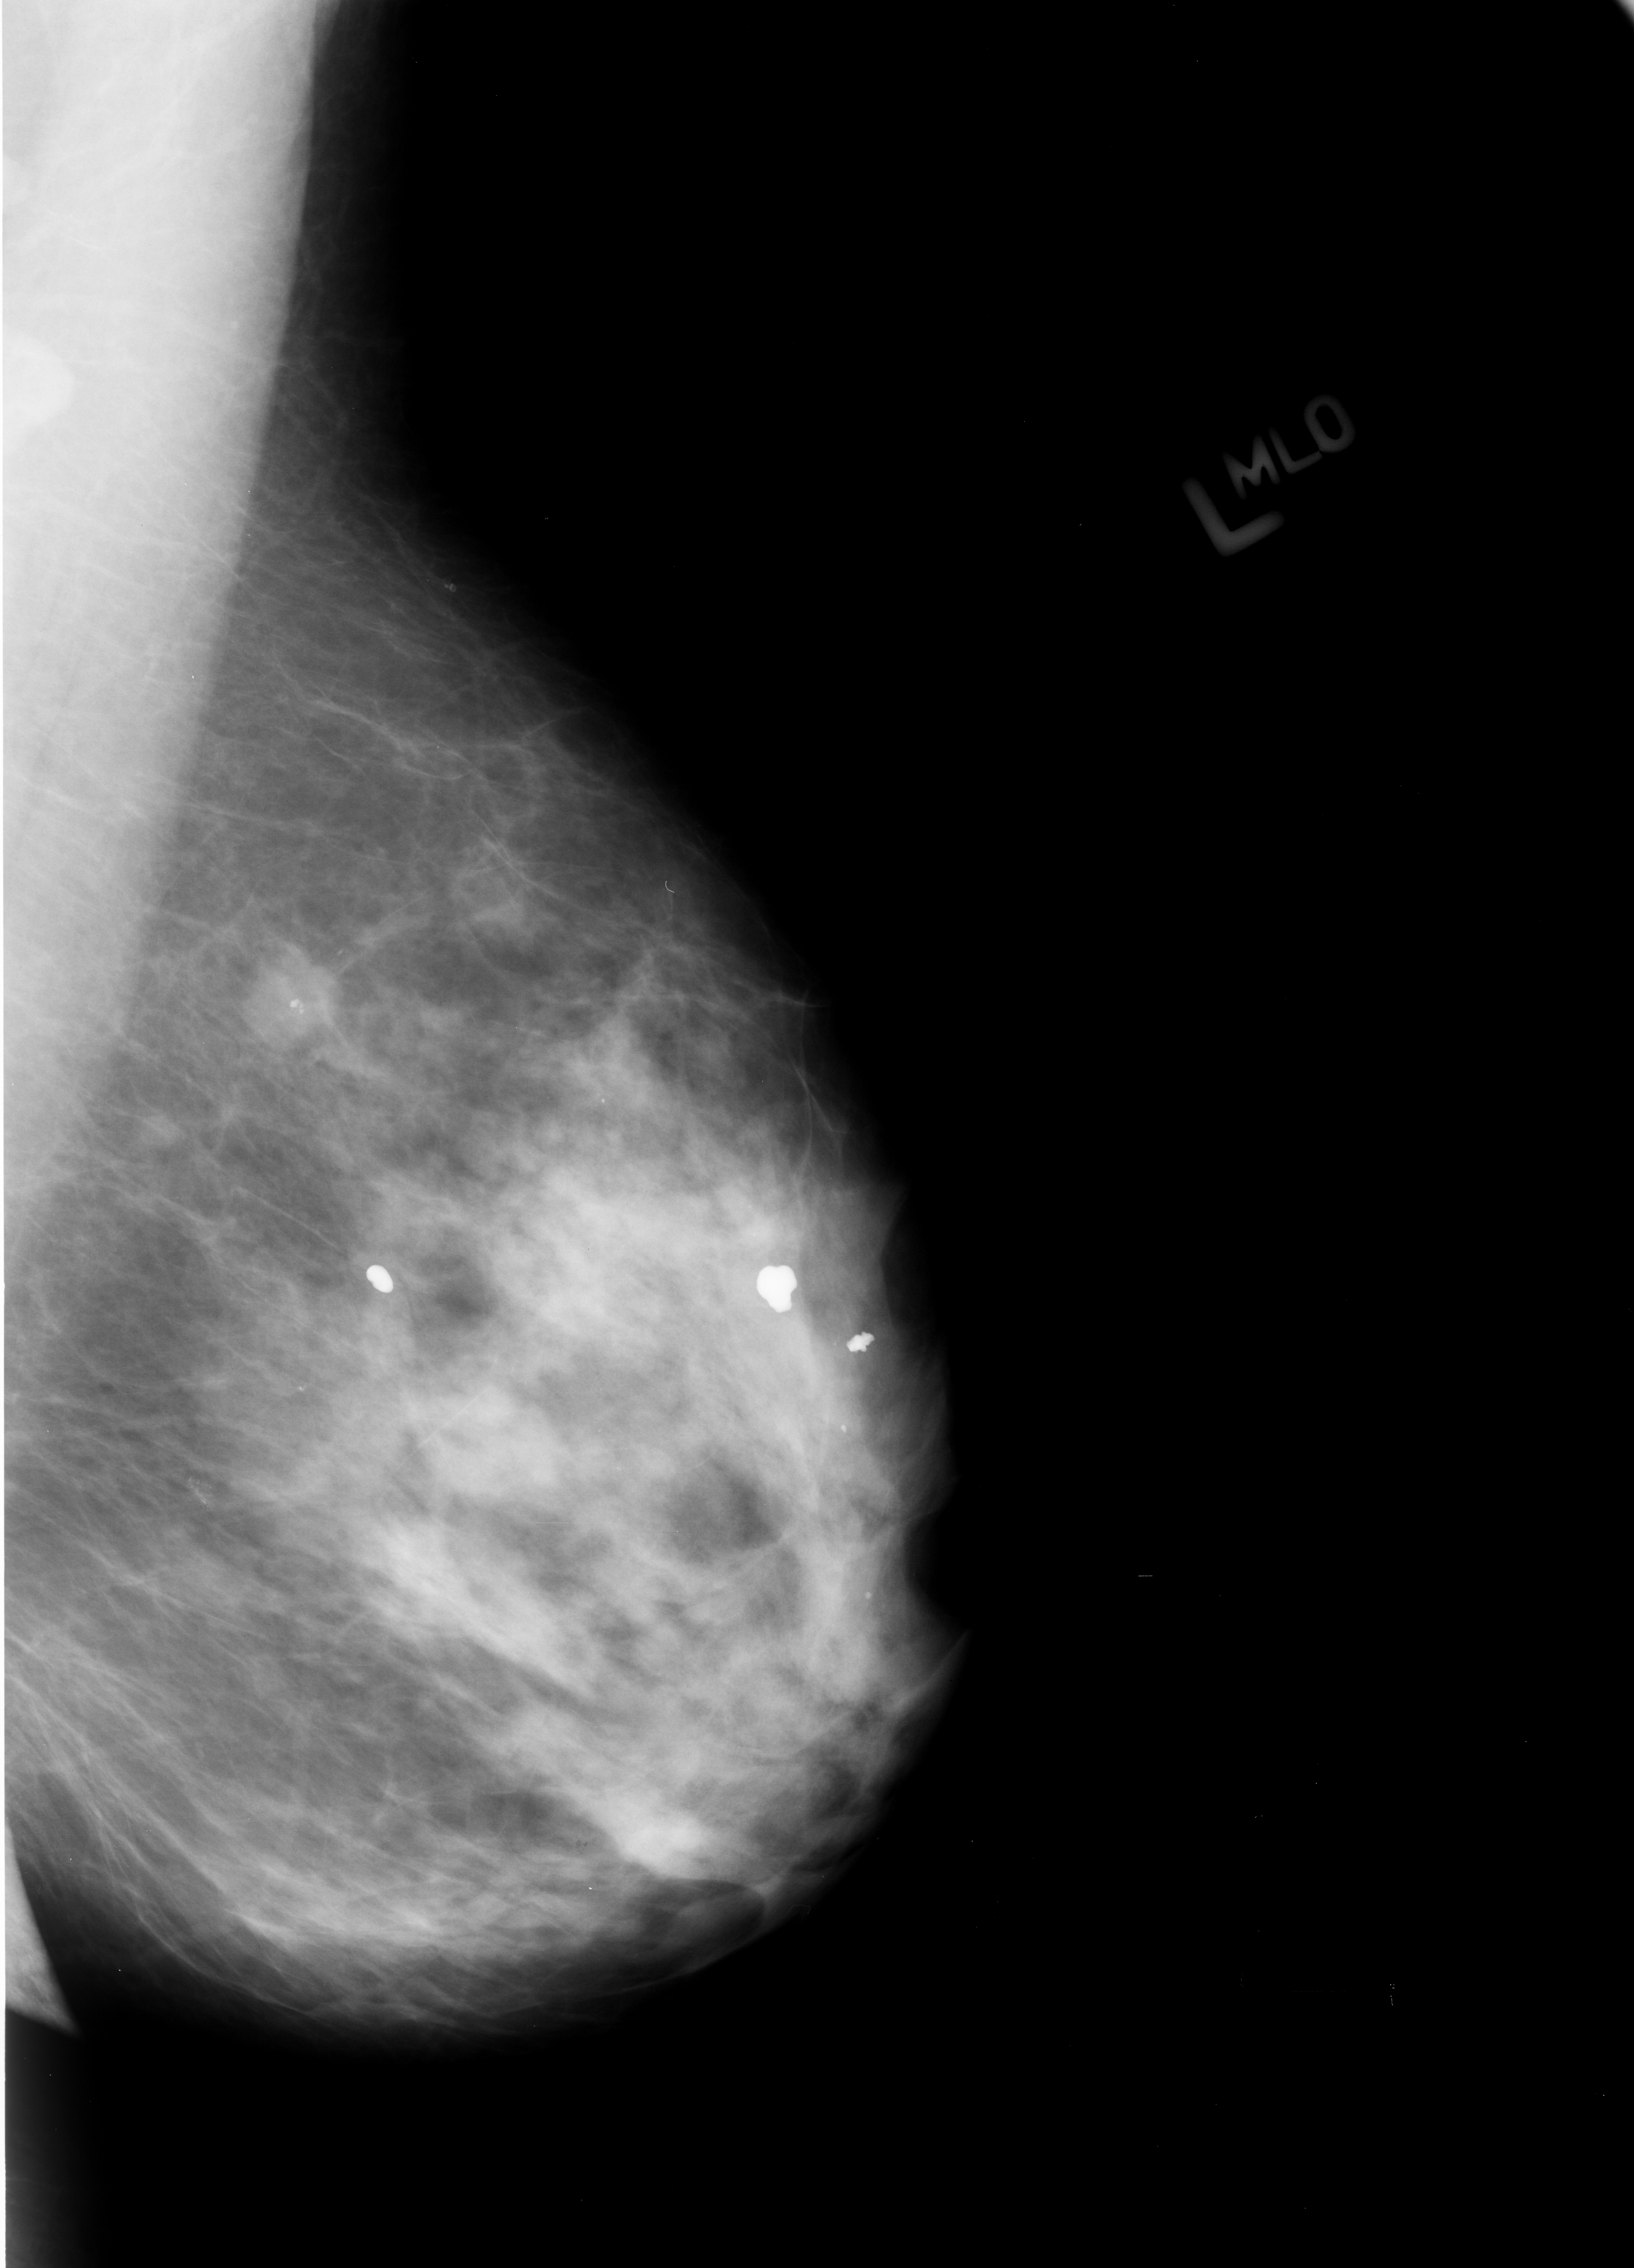
Mammogram (digitized film); left breast; mediolateral oblique (MLO) view.
Abnormality record for this image: mass, shape irregular, margins ill defined / spiculated; BI-RADS assessment category 4; subtlety rating 4 on a 1 (subtle) to 5 (obvious) scale; pathology result (as recorded, not read from the image): malignant.